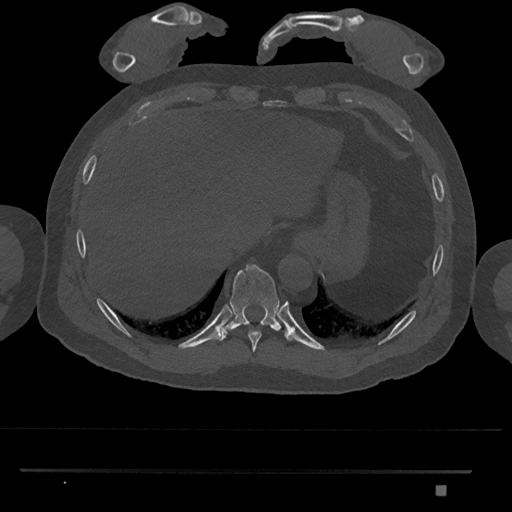
CT including the spine, one axial slice; slice 1021 of 1134 in the series (ordered by position); 120 kVp; bone window (W 1800 / L 400 HU); 0.5 mm slice thickness; 512 × 512 image matrix, field of view 429 × 429 mm. Male patient, age 65 years. From the clinical record (not read from this slice): primary cancer: prostate.
Outlined on this slice (semi-automatic segmentation, software-assisted and operator-edited):
- T10 vertebra: box from (x=219, y=264) to (x=282, y=341) px
- T9 vertebra: (x=248, y=331)–(x=262, y=353)